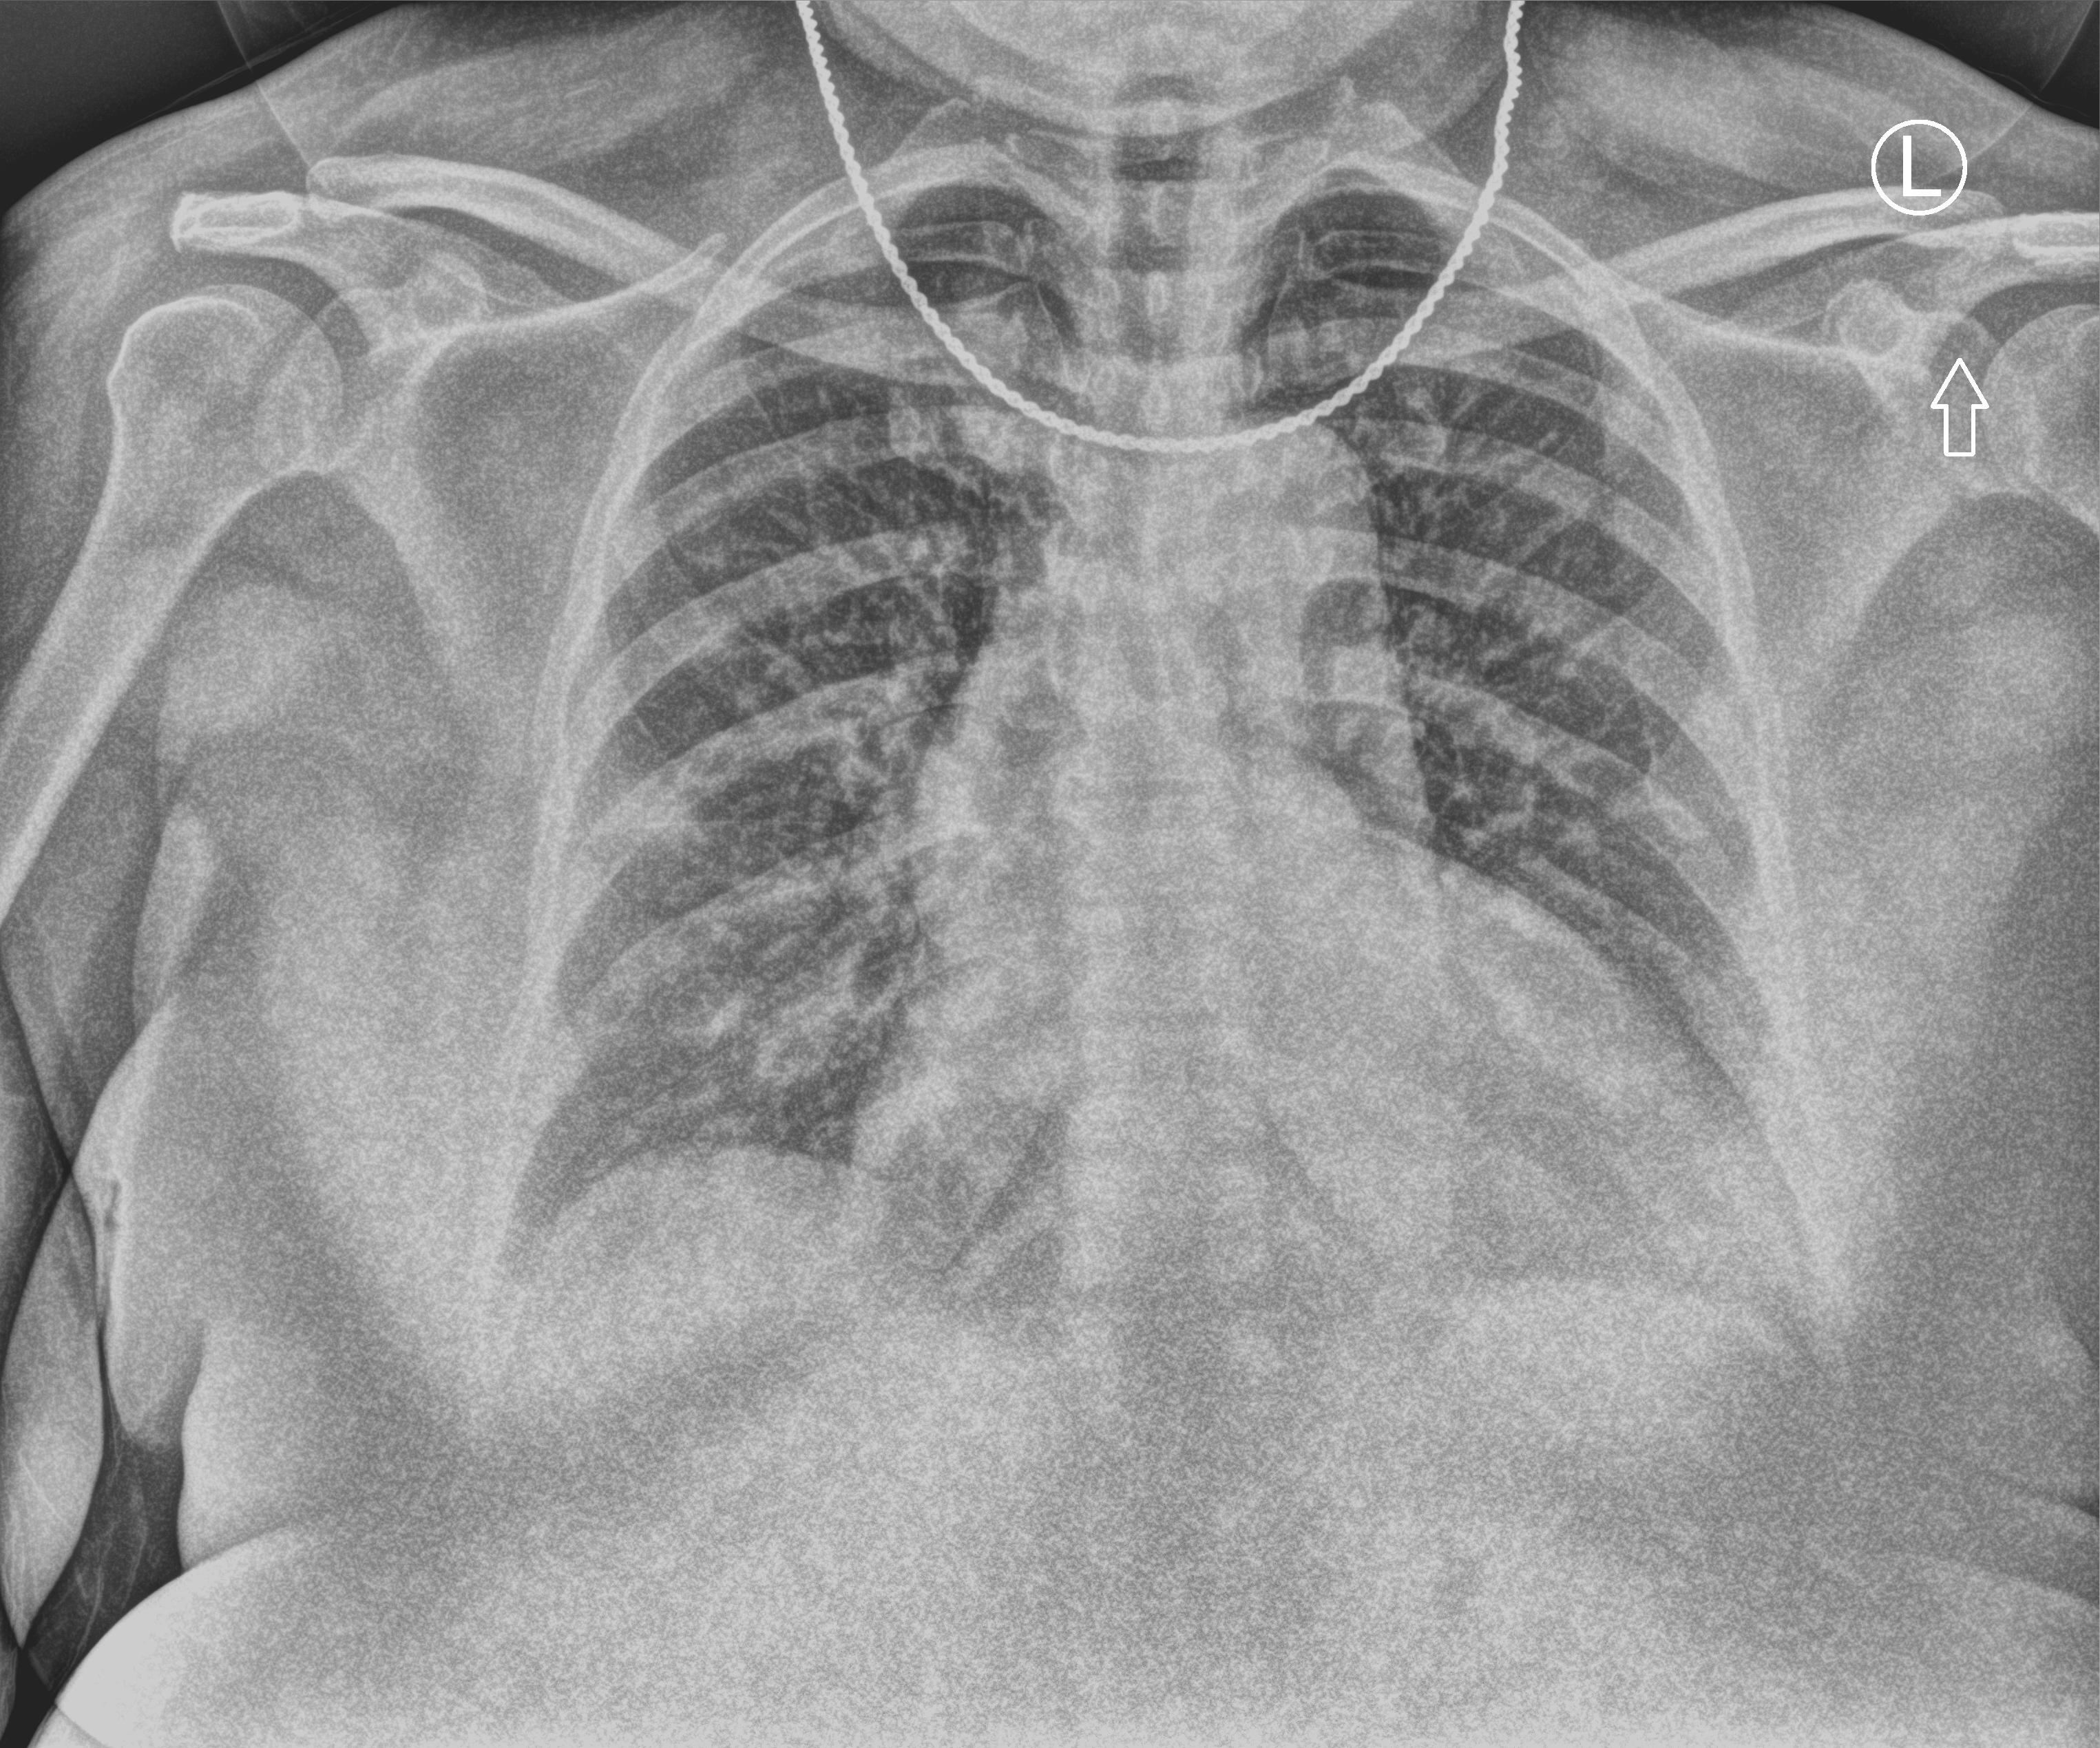
Portable chest radiograph; anteroposterior (AP) projection. Female patient hospitalised with COVID-19, age 60–74 years.
Admission-level facts for this patient (not findings on this image; timing relative to this image not recorded): admitted to intensive care during this hospital stay: yes; mechanically ventilated during this hospital stay: yes.